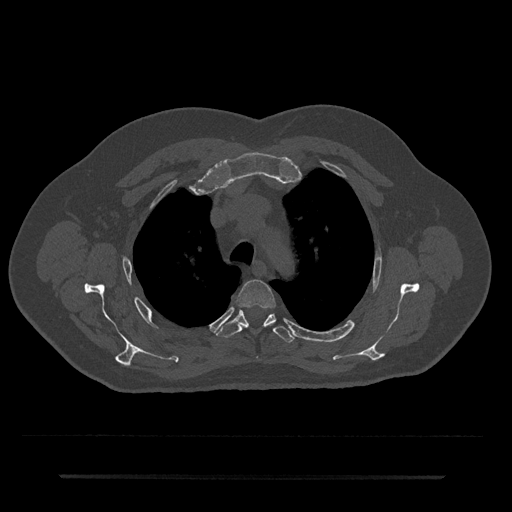
CT including the spine, one axial slice. Slice 546 of 797 in the series (ordered by position). Reconstruction kernel Br40s/3. 120 kVp. Bone window (W 1800 / L 400 HU). 0.5 mm slice thickness. 512 × 512 image matrix. Patient: male, 69 years. From the clinical record (not read from this slice): primary cancer: prostate.
Outlined on this slice (semi-automatic segmentation, software-assisted and operator-edited):
- T3 vertebra: bounding box <237,280,276,308> (left, top, right, bottom; pixels)
- T4 vertebra: <216,309,294,343>